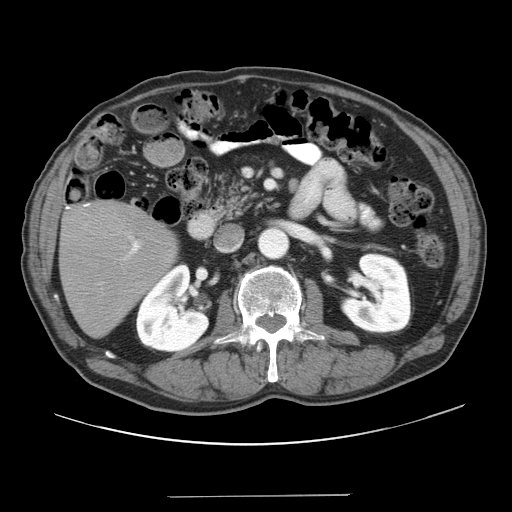
Contrast-enhanced abdominal CT, one axial slice. Slice 14 of 41 in the series (ordered by position). 120 kVp. Intravenous contrast given. Soft-tissue window (W 400 / L 40 HU). 5 mm slice thickness. 512 × 512 image matrix, field of view 420 × 420 mm. Male patient, age 75 years. From the clinical record (not read from this slice): diagnosis: colorectal cancer liver metastases, imaged before liver resection; multiple liver metastases: no; largest metastasis: 5.2 cm; disease in both lobes: no.
Annotated regions visible in this slice (expert manual segmentation):
- liver: bounding box [x1, y1, x2, y2] px = [60, 202, 176, 337]
- planned liver remnant (the part of the liver to remain after resection): [60, 203, 176, 337]
- portal vein (with intrahepatic branches): [123, 234, 141, 260]